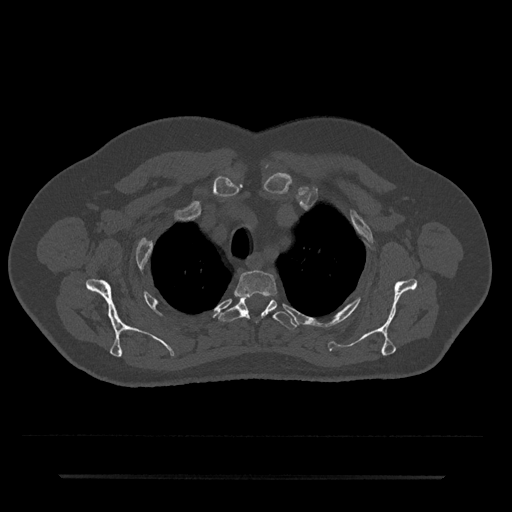
CT including the spine, one axial slice. Position 582 of 797 along the scan axis. Bone window (W 1800 / L 400 HU). 0.5 mm slice thickness. 512 × 512 image matrix, field of view 437 × 437 mm. Patient: male, 69 years. Case-level facts recorded for this patient, not image findings: primary cancer: prostate.
Annotated regions visible in this slice (semi-automatically segmented with operator editing):
- T2 vertebra: box from (x=235, y=270) to (x=277, y=298) px
- T3 vertebra: (x=220, y=298)–(x=298, y=329)